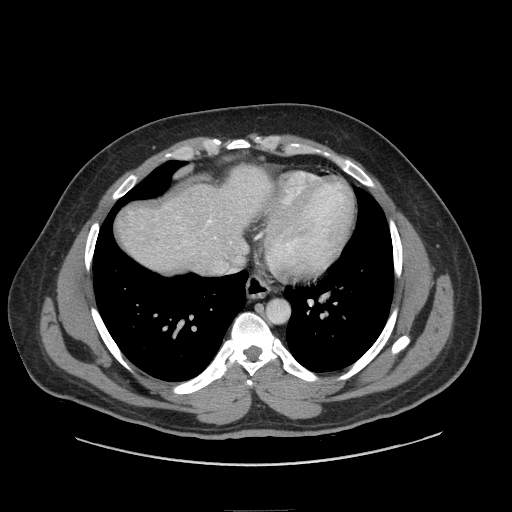
Contrast-enhanced abdominal CT (liver protocol), one axial slice. Position 75 of 87 along the scan axis. 140 kVp. Soft-tissue window (W 400 / L 40 HU). 2.5 mm slice thickness. 512 × 512 image matrix, field of view 440 × 440 mm. Case-level facts recorded for this patient, not image findings: diagnosis: hepatocellular carcinoma (patient treated with transarterial chemoembolisation; whether this scan precedes or follows treatment is not stated here); TNM stage (as recorded): Stage-II; Child-Pugh class: A.
Structures marked on this image (semi-automatically segmented with operator editing):
- abdominal aorta: bounding box <268,301,289,322> (left, top, right, bottom; pixels)
- liver parenchyma outside the tumour (the mass and vessels are separate outlines, so this box may not span the whole liver): <116,170,263,272>
- liver vessels: <207,220,211,223>